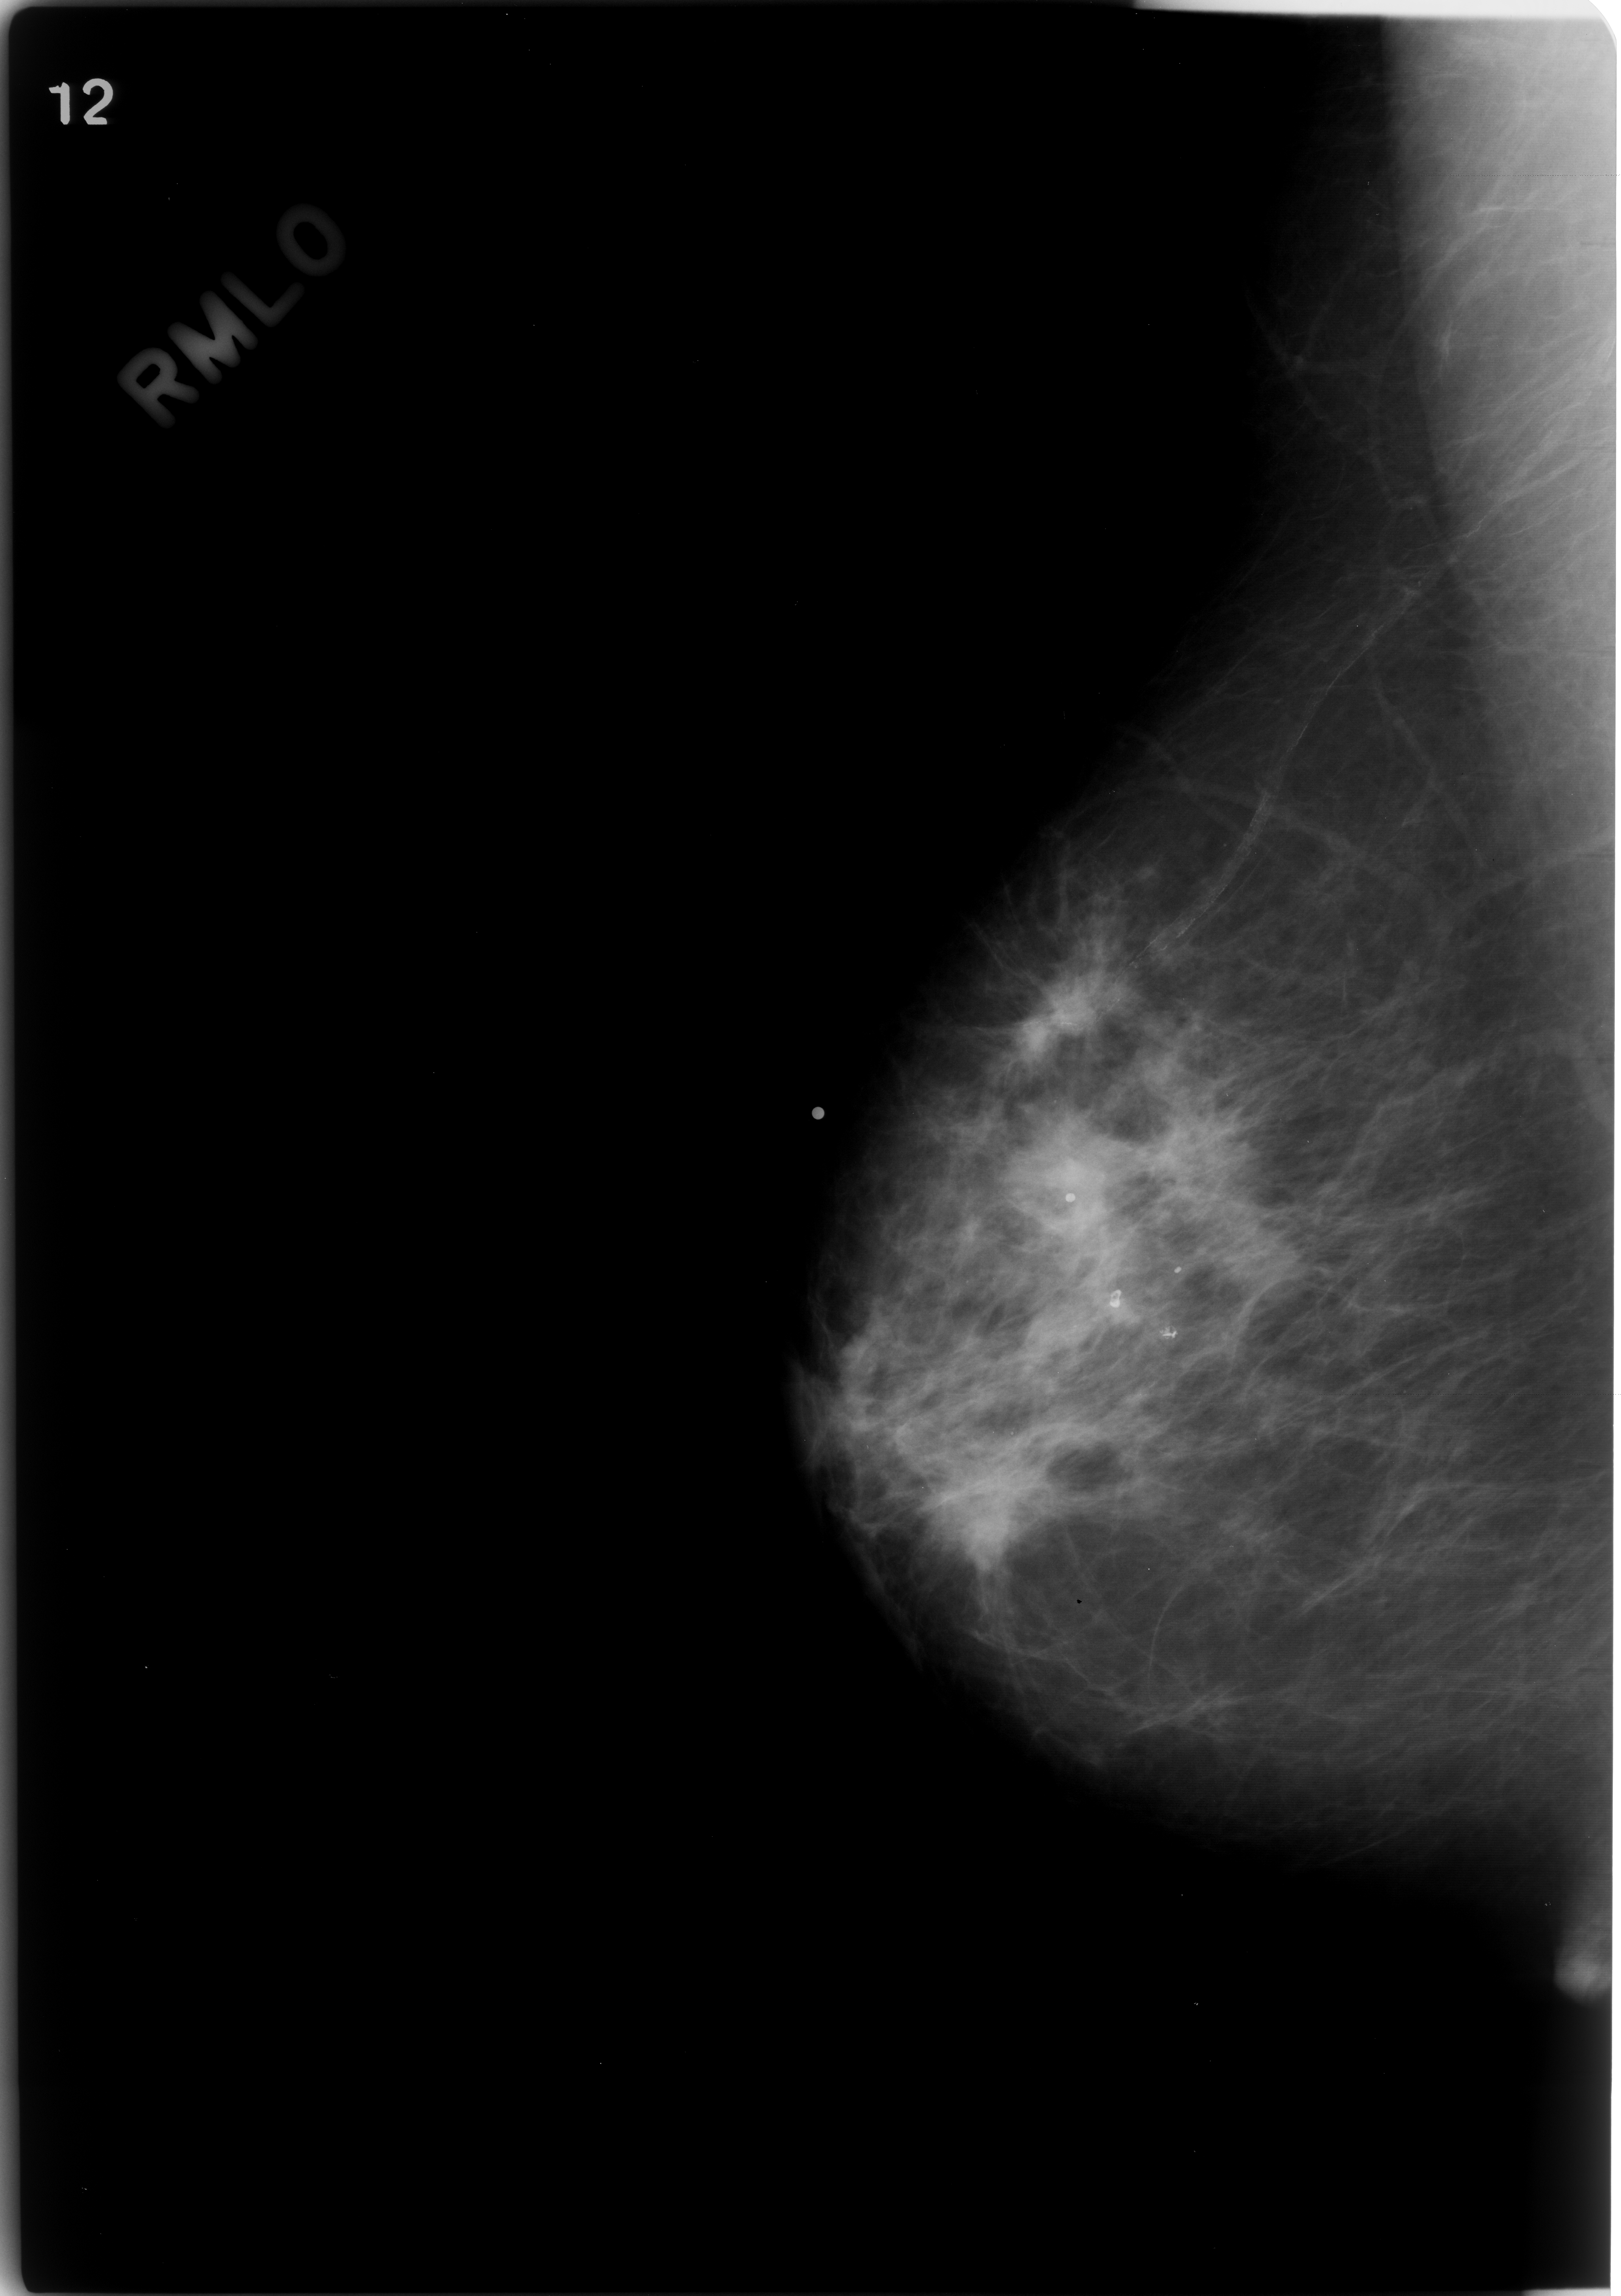
Scanned film-screen mammogram; right breast; MLO view; BI-RADS breast density category 2 (scale 1–4); 1621 × 2296 image matrix.
Marked abnormalities (boxes around the expert regions of interest):
- mass, shape asymmetric breast tissue, margins ill defined; BI-RADS assessment category 5; pathology result (as recorded, not read from the image): malignant: bounding box (x1, y1, x2, y2) in pixels: (948, 1007, 1185, 1329)